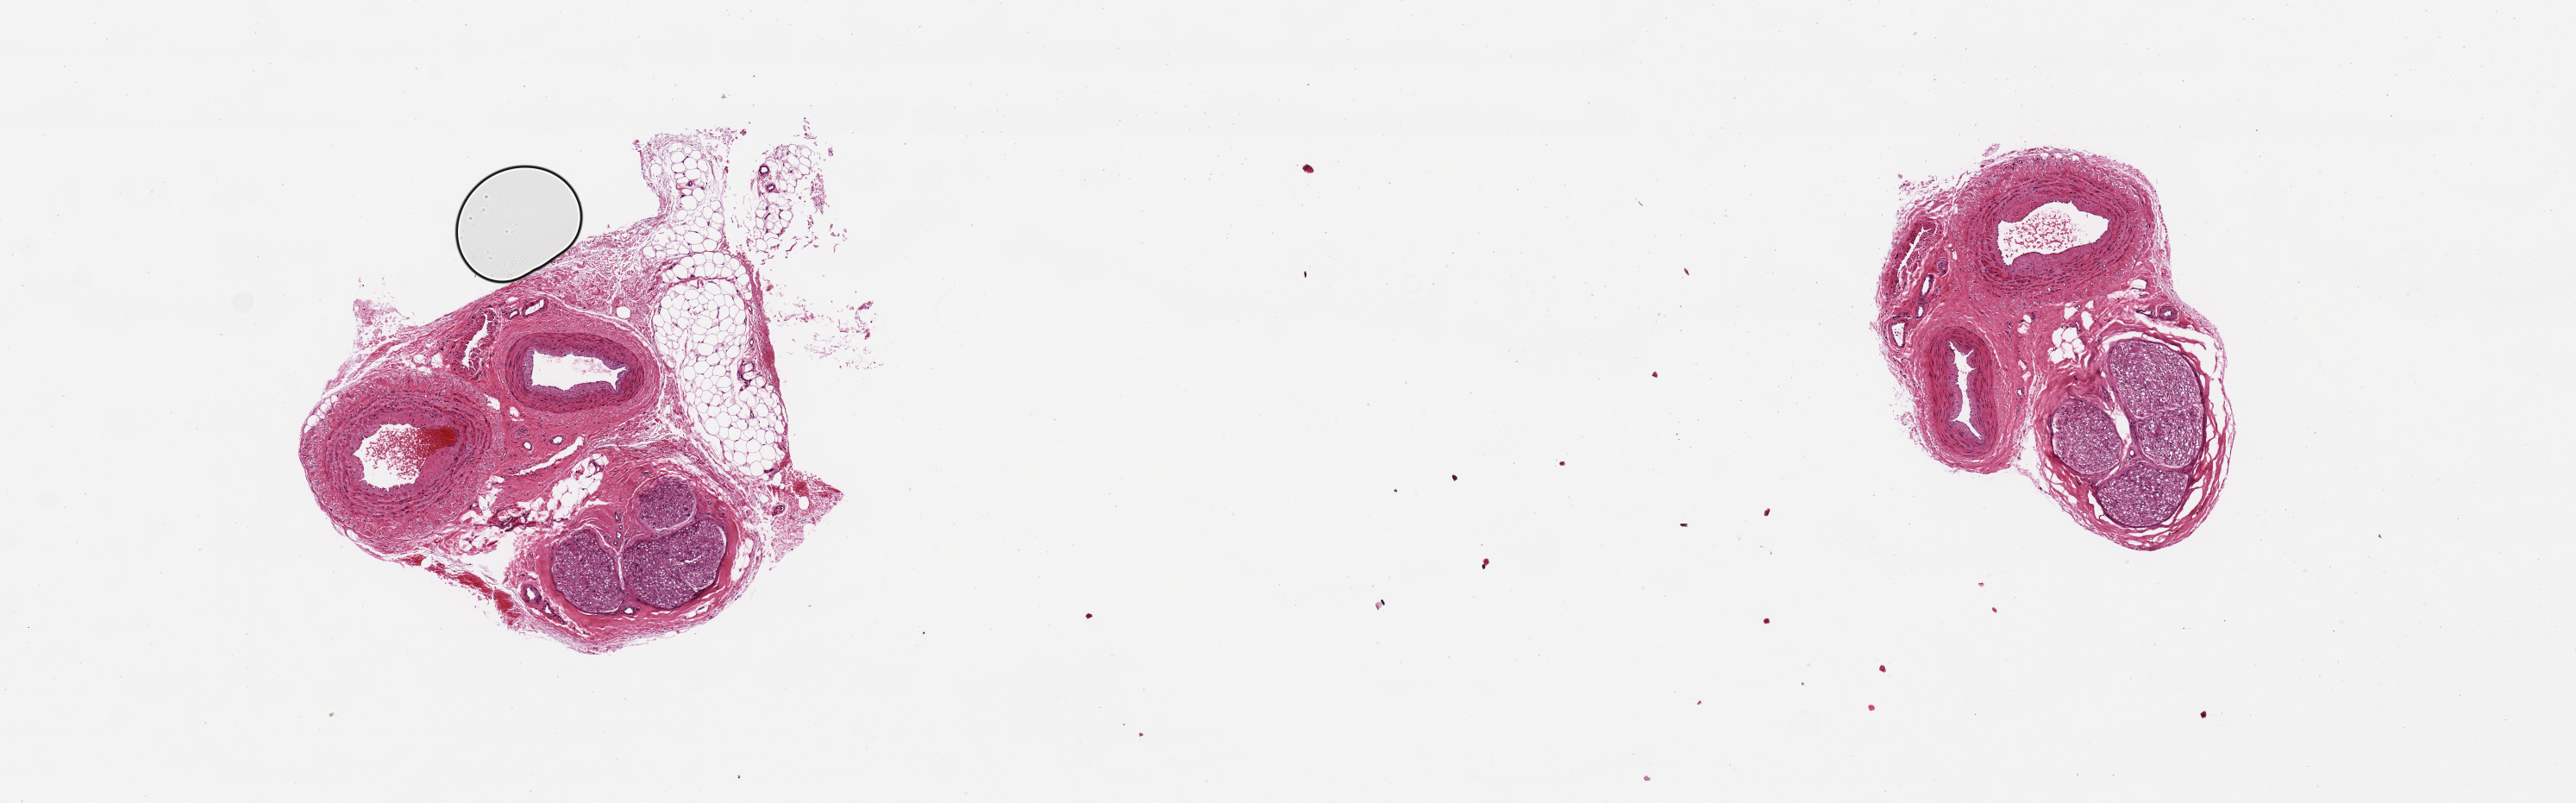
Digitized hematoxylin and eosin (H&E)-stained section, brightfield, low-resolution overview of the scanned area, about 11.8 x 3.7 mm, PAXgene-fixed paraffin-embedded (PFPE) section, sampled site (target tissue): tibial artery, tissue donor sample. Donor: female.
Reviewer comment on this tissue sample: Artery, vein, nerve.